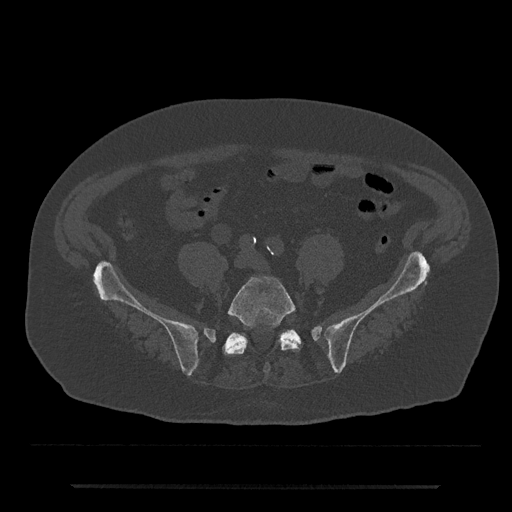
CT including the spine, one axial slice; slice 274 of 797 in the series (ordered by position); 120 kVp; bone window (W 1800 / L 400 HU); 0.5 mm slice thickness; 512 × 512 image matrix, field of view 434 × 434 mm. Male patient, age 80 years. Case-level facts recorded for this patient, not image findings: primary cancer: prostate.
Annotated regions visible in this slice (semi-automatic segmentation, software-assisted and operator-edited):
- L5 vertebra: bounding box [x1, y1, x2, y2] px = [223, 277, 300, 373]